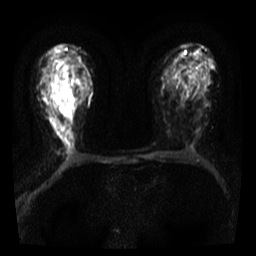
Breast MRI, one axial slice. Slice 22 of 36 in the series (ordered by position). Diffusion-weighted series; image 2 of 4 stored at this slice position (different b-values; order by instance number). 3 T. 5 mm slice thickness. 256 × 256 image matrix, field of view 300 × 300 mm. Female patient.
Annotated regions visible in this slice (expert manual segmentation):
- tumour on diffusion-weighted imaging: box from (x=57, y=69) to (x=69, y=107) px